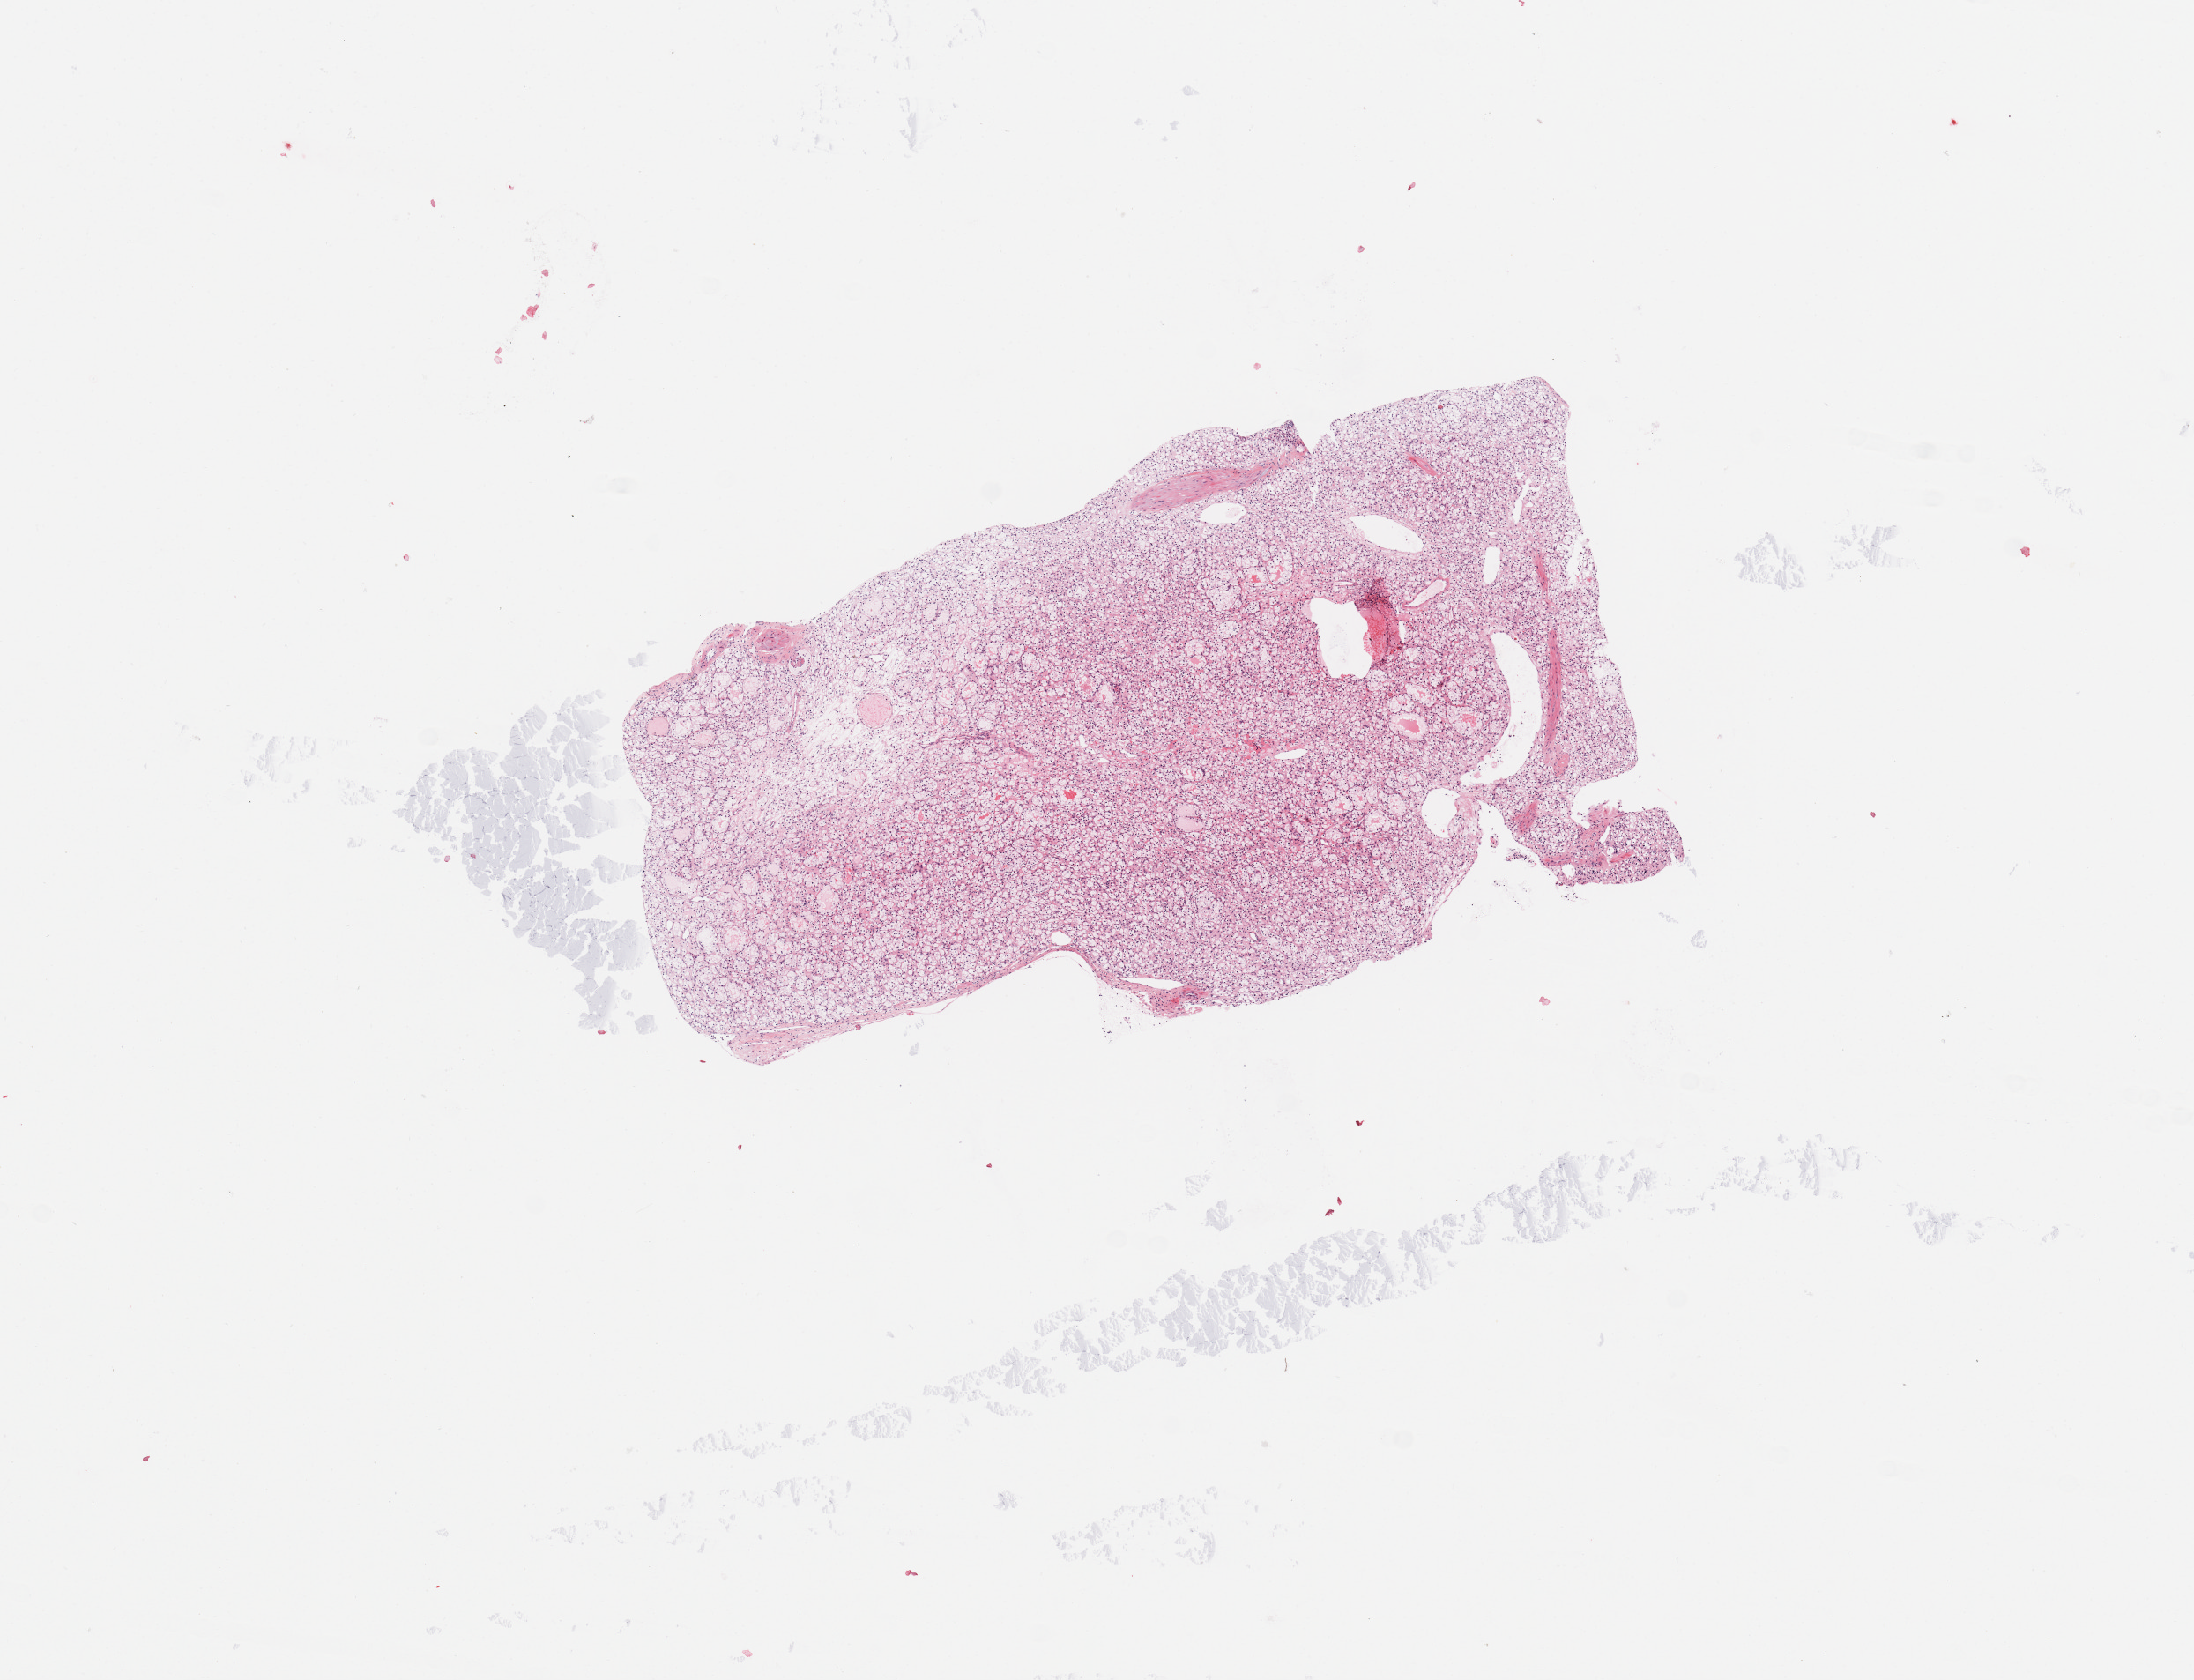
Whole-slide histology image, Hematoxylin and eosin (H&E) stained, shown as a low-resolution overview of the whole scanned area (about 9.8 x 7.5 mm, from a 20x scan); tumour tissue sample, sampled site: kidney. Patient: female, age 47 years. Pathologist review of this section (percent, as recorded): tumour nuclei 90%, necrosis 2%.
Diagnosis: Renal cell carcinoma, NOS.